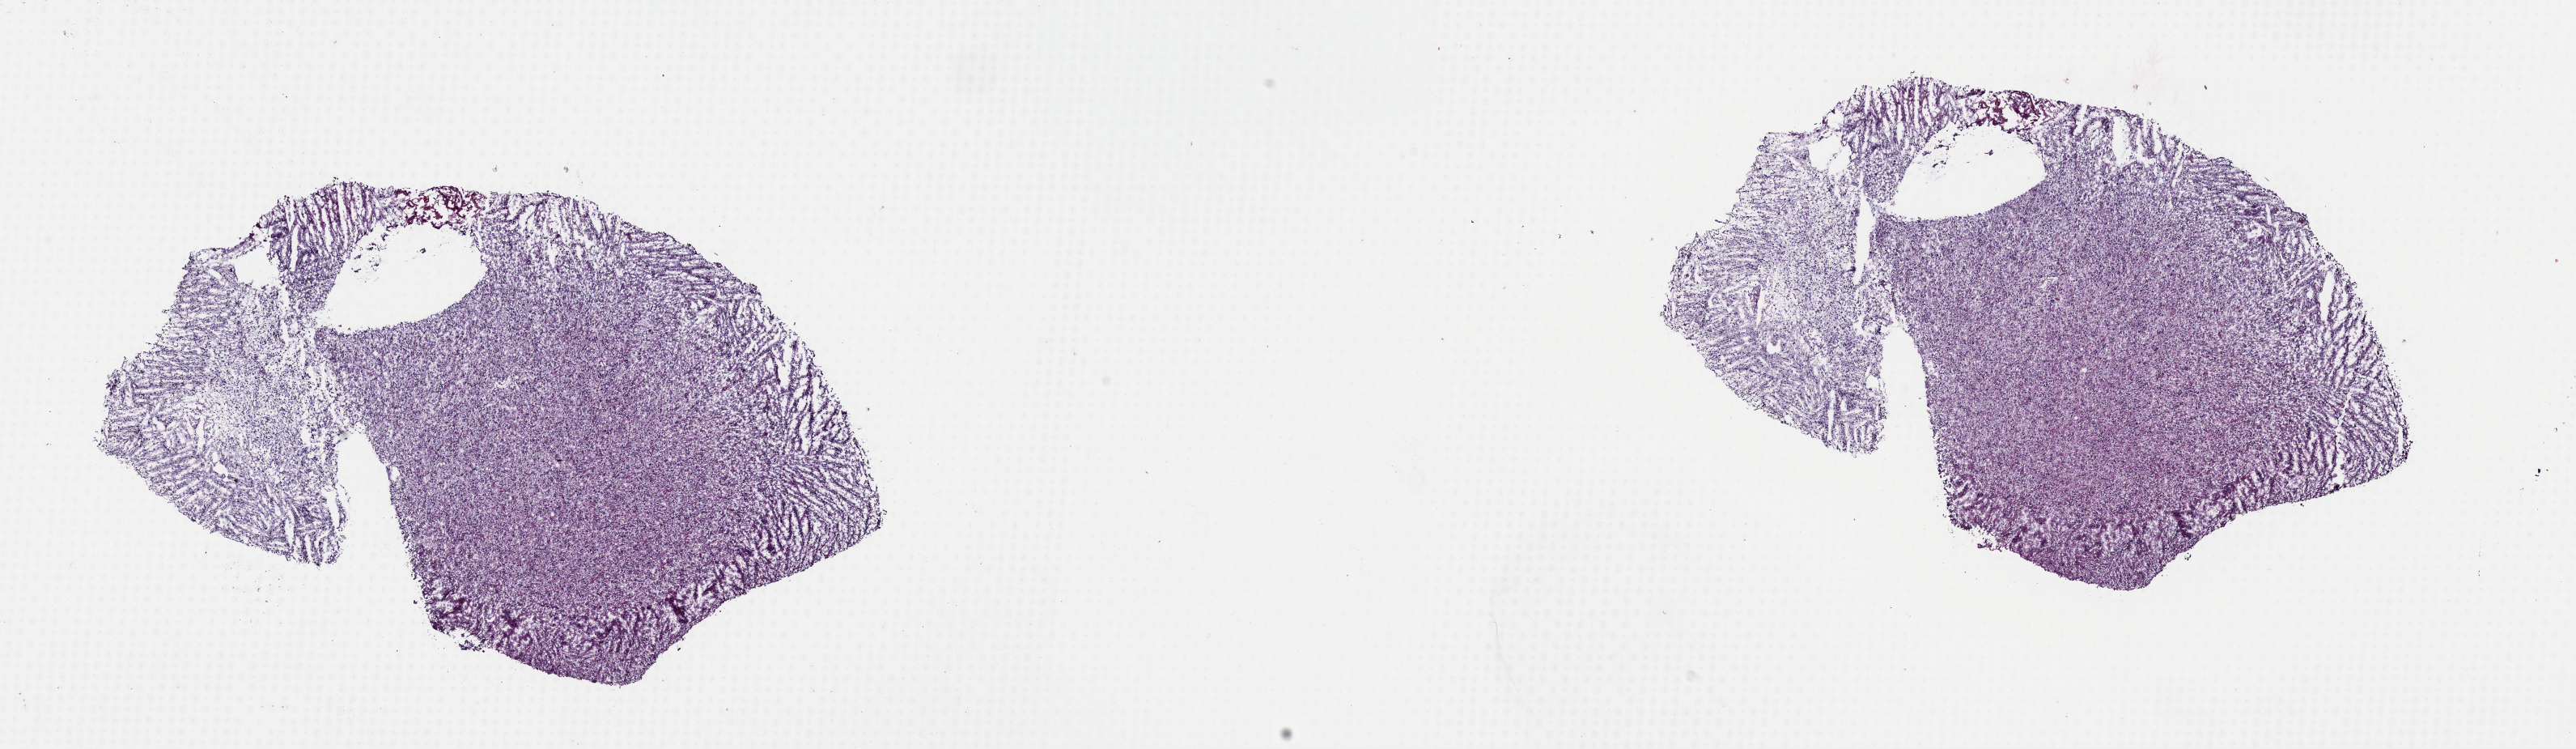
Whole-slide histology image, H&E — whole scanned area (about 25.1 x 7.3 mm, slide scanned at 40x) shown as a low-resolution overview; frozen section; brain, primary tumour sample. Patient: male, age at initial diagnosis 62 years. Histologic grade: G3 (poorly differentiated). Composition of this section per pathologist review: tumour cells 90%, tumour nuclei 90%, normal cells 5%, stromal cells 5%, necrosis 0%. Inflammatory infiltration, as recorded: lymphocyte infiltration 5%, monocyte infiltration 0%, neutrophil infiltration 0%.
Laterality: left. Pathologic diagnosis: Astrocytoma, anaplastic (cerebrum).